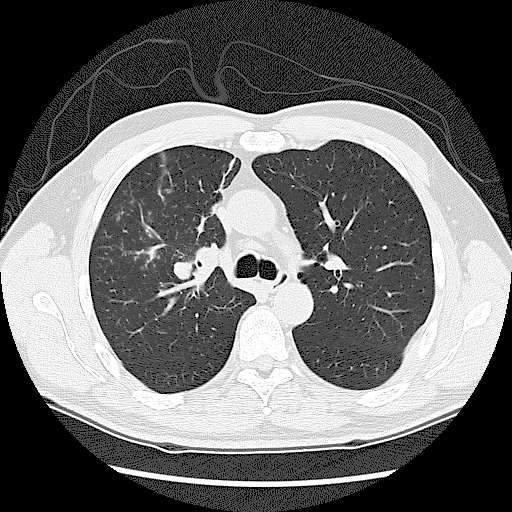
Chest CT (low-dose screening protocol), one axial image, first (baseline) screen, lung window (W 1500 / L -600 HU), 120 kVp, 512 × 512 image matrix. Male participant, aged 60 years at enrolment. Current smoker at enrolment.
Lesion marked by an expert reader, bounding box (x1, y1, x2, y2) in pixels: (159, 223, 244, 318). Screening reader's record for this exam: no non-calcified nodule ≥4 mm recorded.